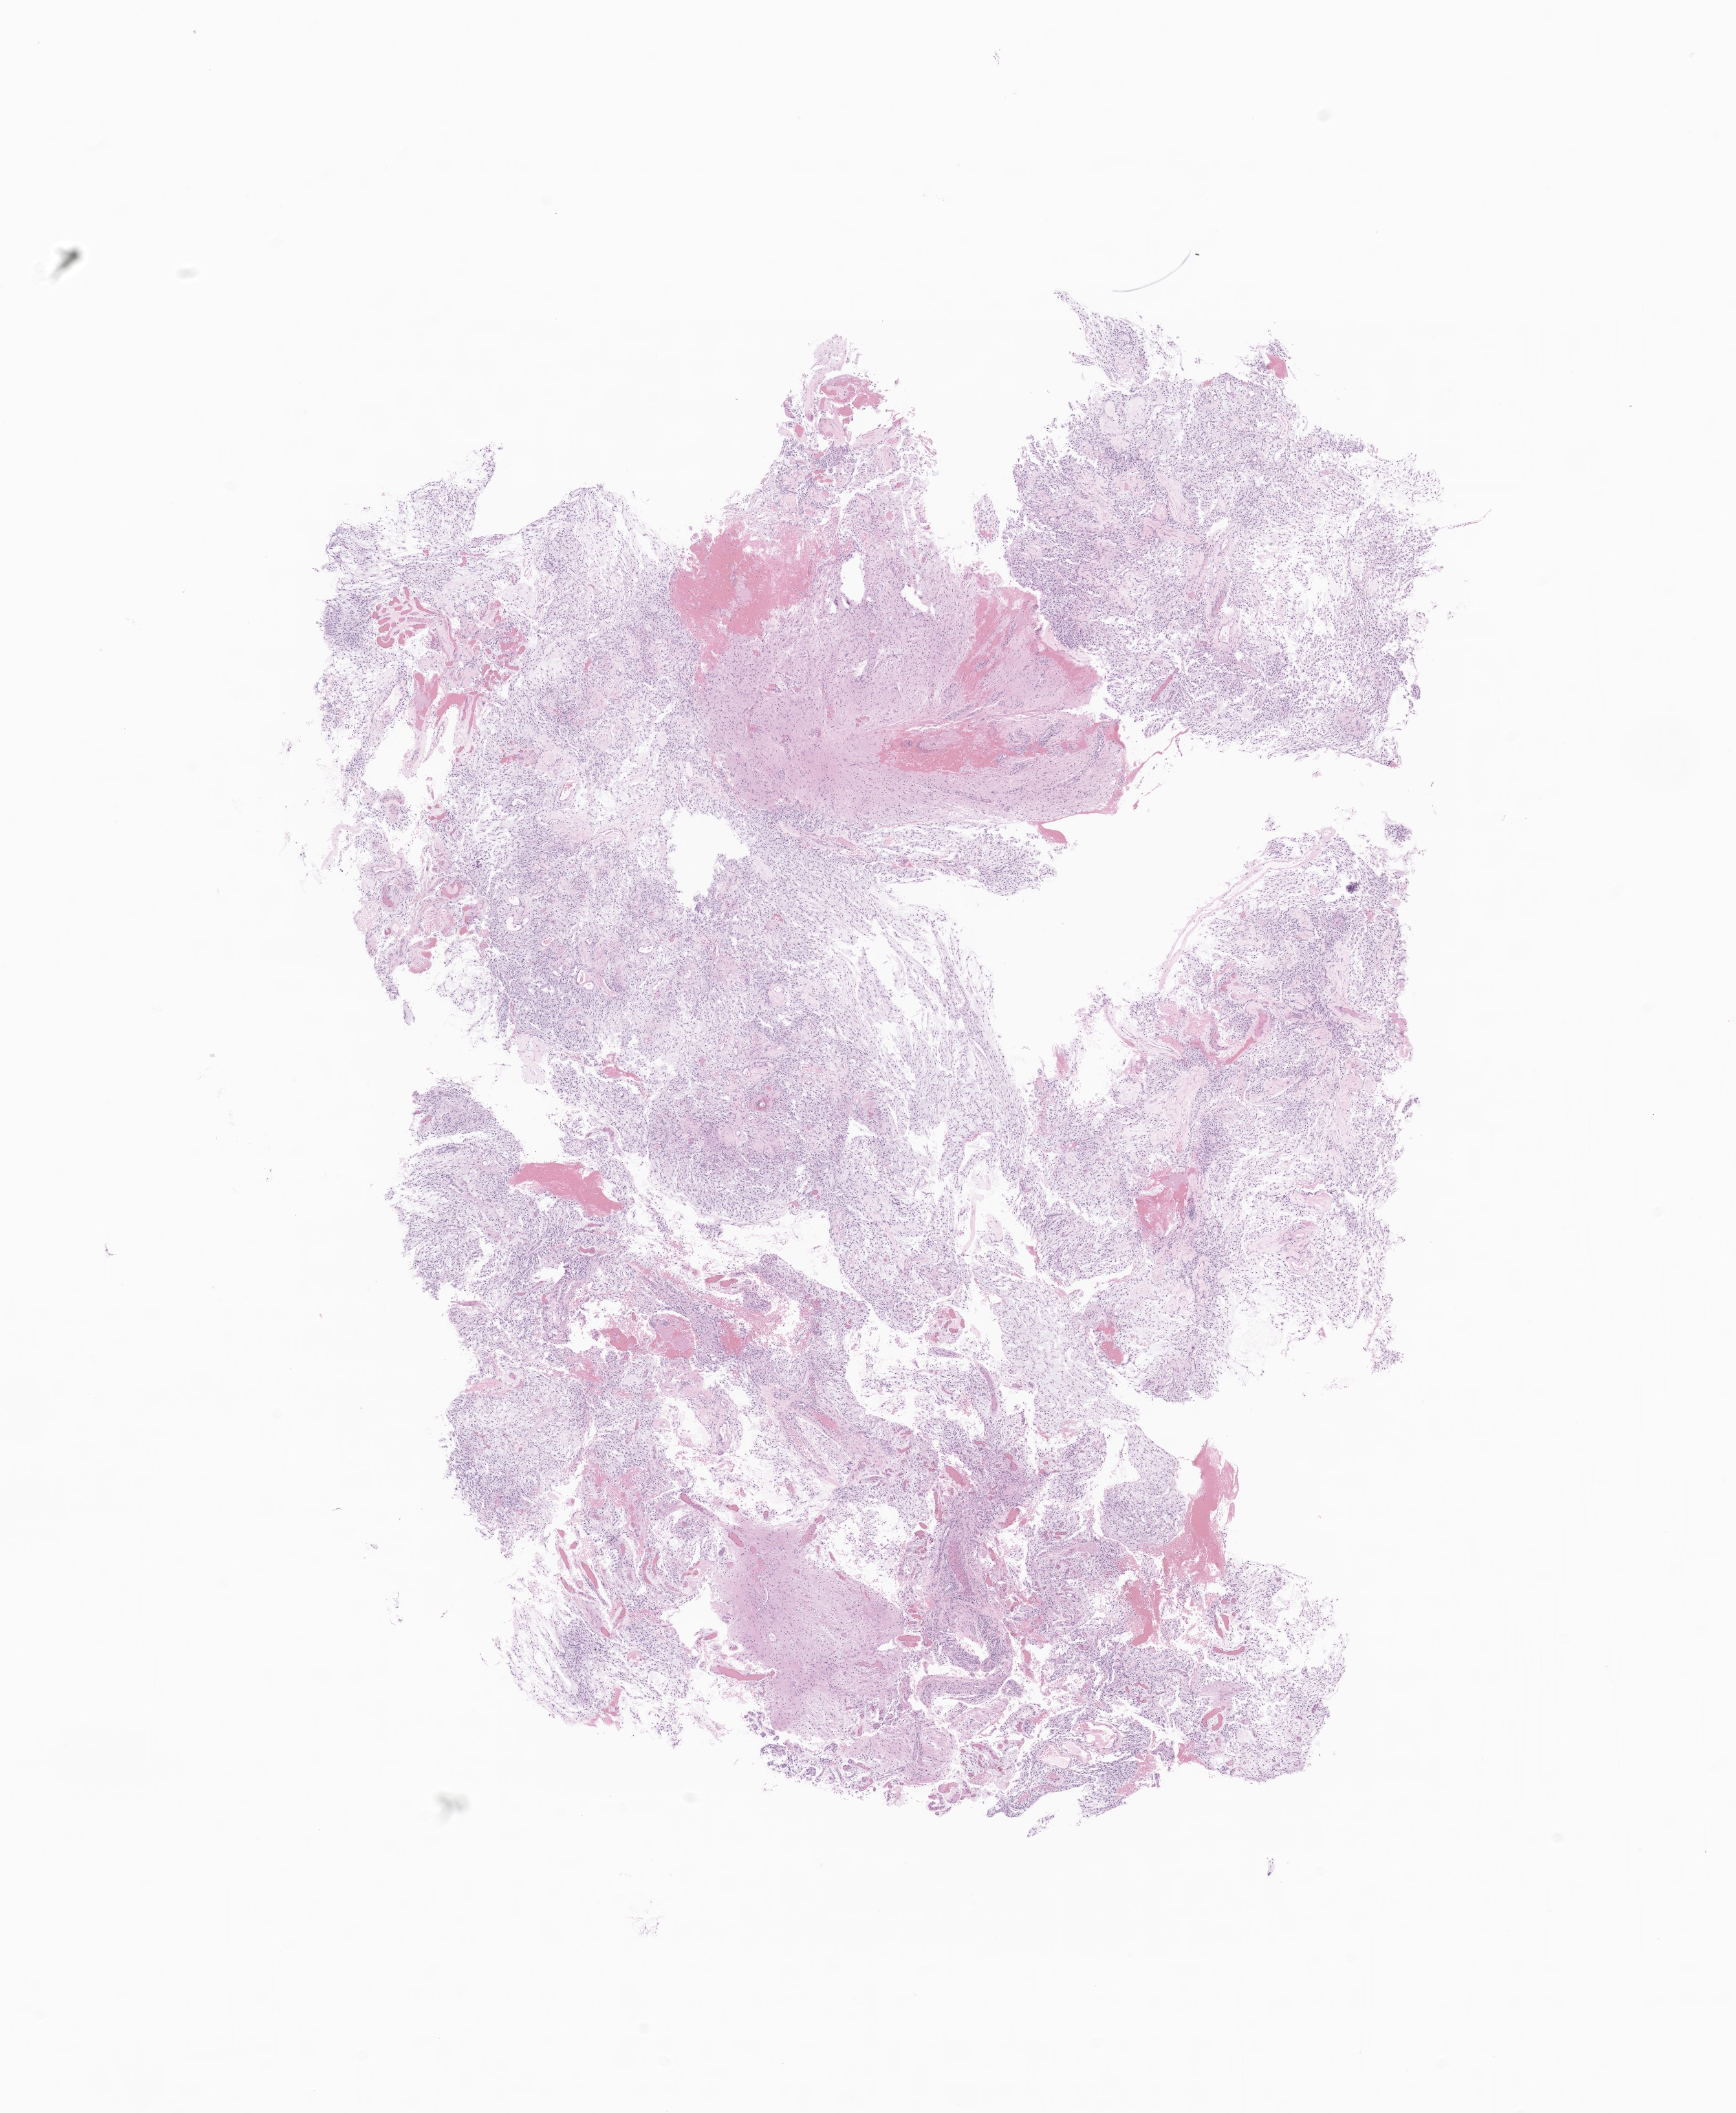
Hematoxylin and eosin (H&E) whole-slide image of tumor tissue from the spinal cord — low-resolution overview of the scanned area, about 11.3 x 13.8 mm, formalin-fixed paraffin-embedded section. Patient male; age 69 months (5 years 9 months).
Recorded diagnosis: Pilocytic astrocytoma.